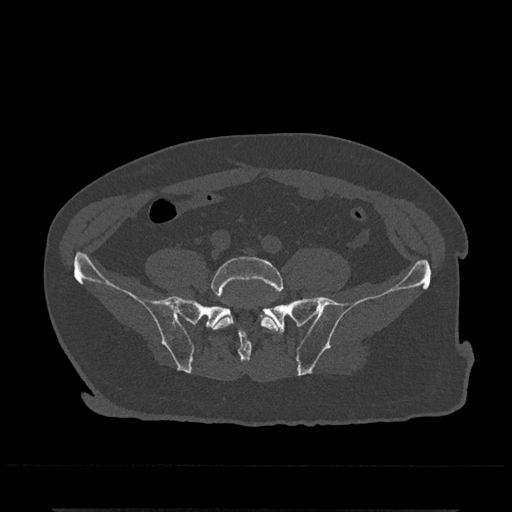
CT including the spine, one axial slice; position 56 of 797 along the scan axis; reconstruction kernel Br40s/3; bone window (W 1800 / L 400 HU); 0.5 mm slice thickness; 512 × 512 image matrix, field of view 393 × 393 mm. Patient: male, 67 years. From the clinical record (not read from this slice): primary cancer: prostate.
Structures marked on this image (semi-automatically segmented with operator editing):
- L5 vertebra: box from (x=208, y=256) to (x=283, y=332) px